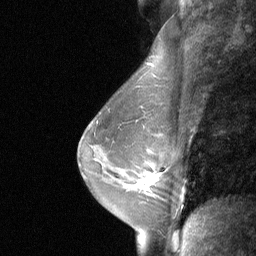
Breast MRI (dynamic contrast-enhanced), one sagittal slice; slice 43 of 64 in the series (ordered by position); dynamic contrast-enhanced study with each time point stored as its own series, time point 2 of 3 at this slice position (early post-contrast, ordered by acquisition time); 1.5 T; TE 4.8 ms, TR 27 ms; 2 mm slice thickness; 256 × 256 image matrix. Patient: female, 48 years. From the clinical record (not read from this slice): setting: breast cancer imaged before/during neoadjuvant chemotherapy; receptor status: HR-positive, HER2-negative.
Annotated regions visible in this slice (semi-automatic segmentation, software-assisted and operator-edited):
- analysis volume of interest (the breast-tissue region the enhancement analysis was run in; not a lesion): bounding box (x1, y1, x2, y2) in pixels: (131, 165, 170, 200)
- tumour enhancement mask (voxels above the 90 % enhancement threshold inside the analysis volume of interest): (143, 175, 158, 190)